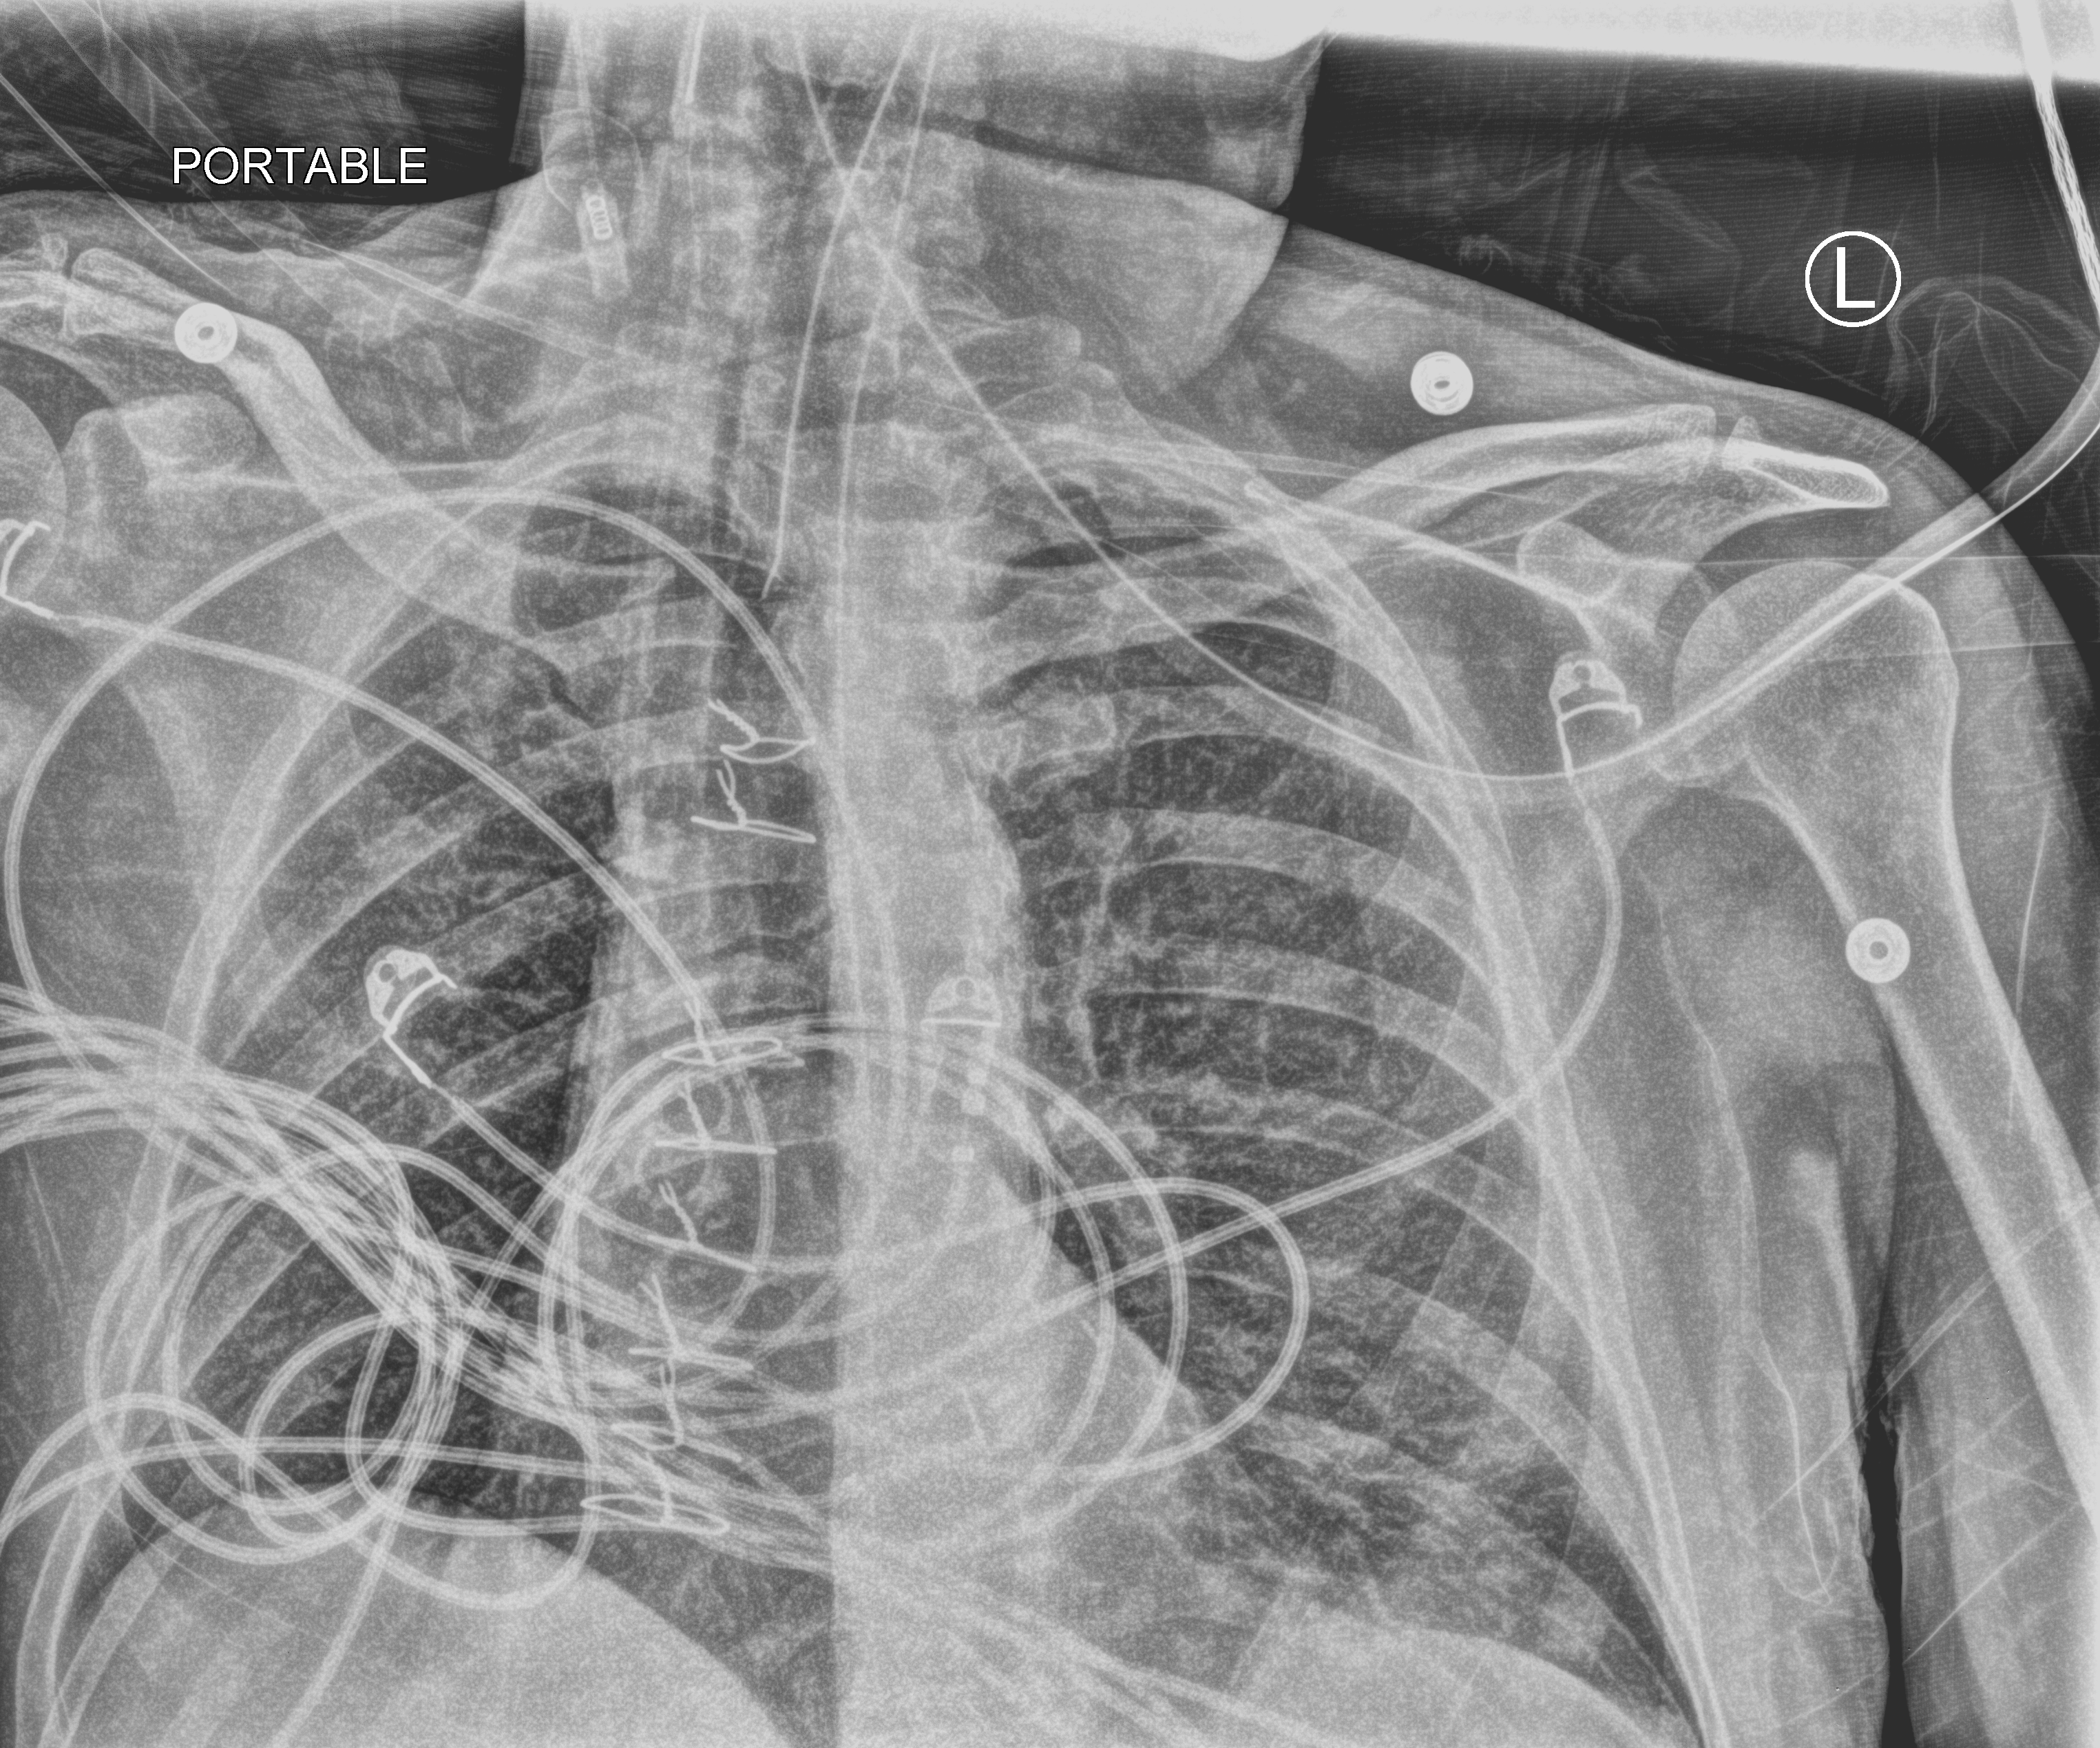
Bedside chest radiograph (computed radiography). Patient hospitalised with COVID-19; male, aged 18–59 years.
Admission-level facts for this patient (not findings on this image; timing relative to this image not recorded):
- diabetes (admission record): yes